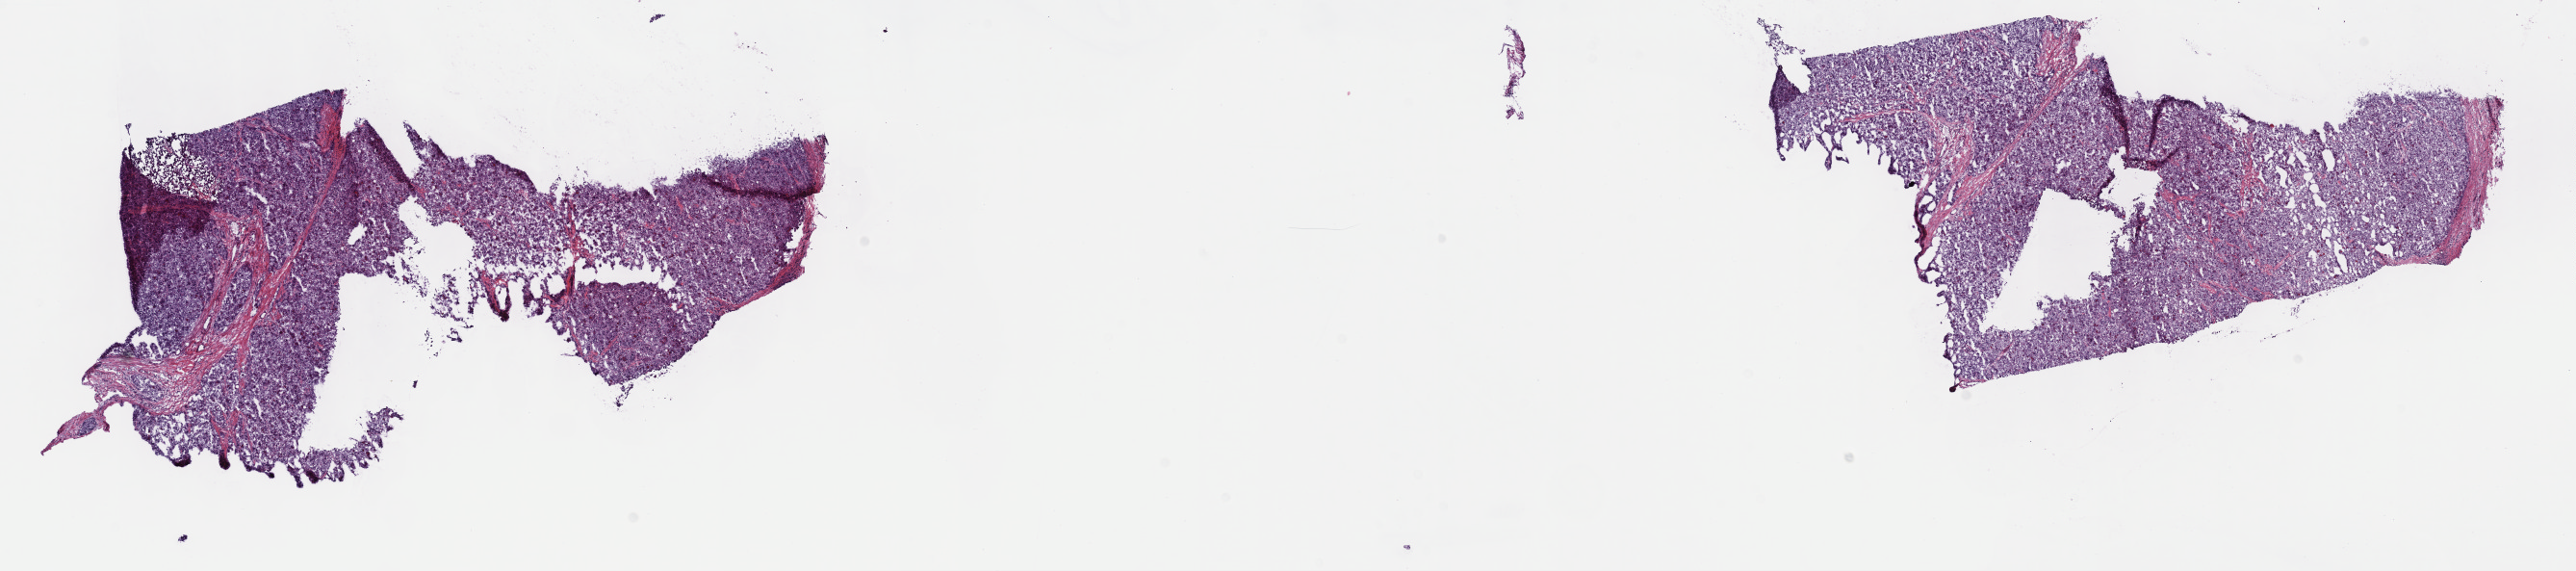
Digitized Hematoxylin and eosin (H&E) stained tissue section (whole slide), a low-resolution overview of the entire scanned area, about 21.6 x 4.8 mm; frozen section from the top of the tissue portion; sample: primary tumour, liver. Male patient; age at initial diagnosis 64 years. Histologic grade: G2 (moderately differentiated). Composition of this section per pathologist review: tumour cells 100%, tumour nuclei 95%, normal cells 0%, stromal cells 0%, necrosis 0%. Inflammatory infiltration, as recorded: lymphocyte infiltration 0%, monocyte infiltration 0%, neutrophil infiltration 0%.
Pathologic diagnosis: Hepatocellular carcinoma, NOS. AJCC pathologic stage: I (6th edition). TNM: T1 N0 MX.